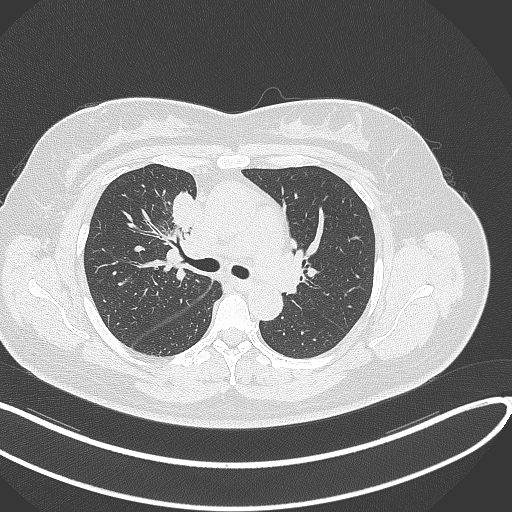
Chest CT, one axial slice. Position 177 of 303 along the scan axis. Reconstruction kernel B70f. 120 kVp. Lung window (W 1500 / L -600 HU). 1 mm slice thickness. 512 × 512 image matrix, field of view 400 × 400 mm. Female patient, age 46 years. From the clinical record (not read from this slice): clinical TNM (as recorded): T2a N1 M0.
Annotated regions visible in this slice (bounding box drawn by a radiologist):
- lung tumour (recorded histology: adenocarcinoma): bounding box [x1, y1, x2, y2] px = [166, 191, 208, 236]